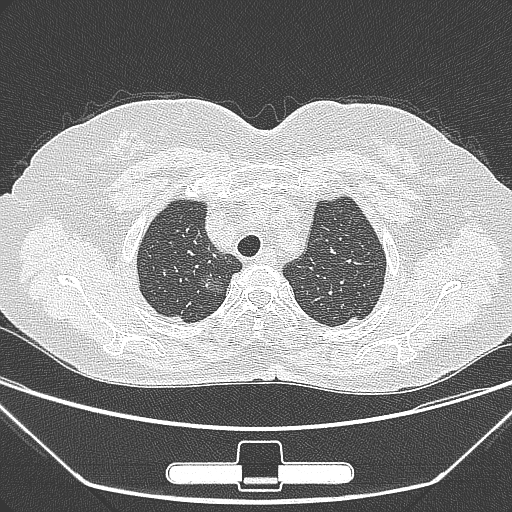
Chest CT, one axial slice. Slice 233 of 275 in the series (ordered by position). 120 kVp. Lung window (W 1500 / L -600 HU). 1 mm slice thickness. 512 × 512 image matrix, field of view 356 × 356 mm. Female patient, age 63 years. Case-level facts recorded for this patient, not image findings: clinical TNM (as recorded): T1a N0 M0.
Outlined on this slice (rectangle marked by the reading radiologist):
- lung tumour (recorded histology: adenocarcinoma): bounding box [x1, y1, x2, y2] px = [197, 268, 226, 295]